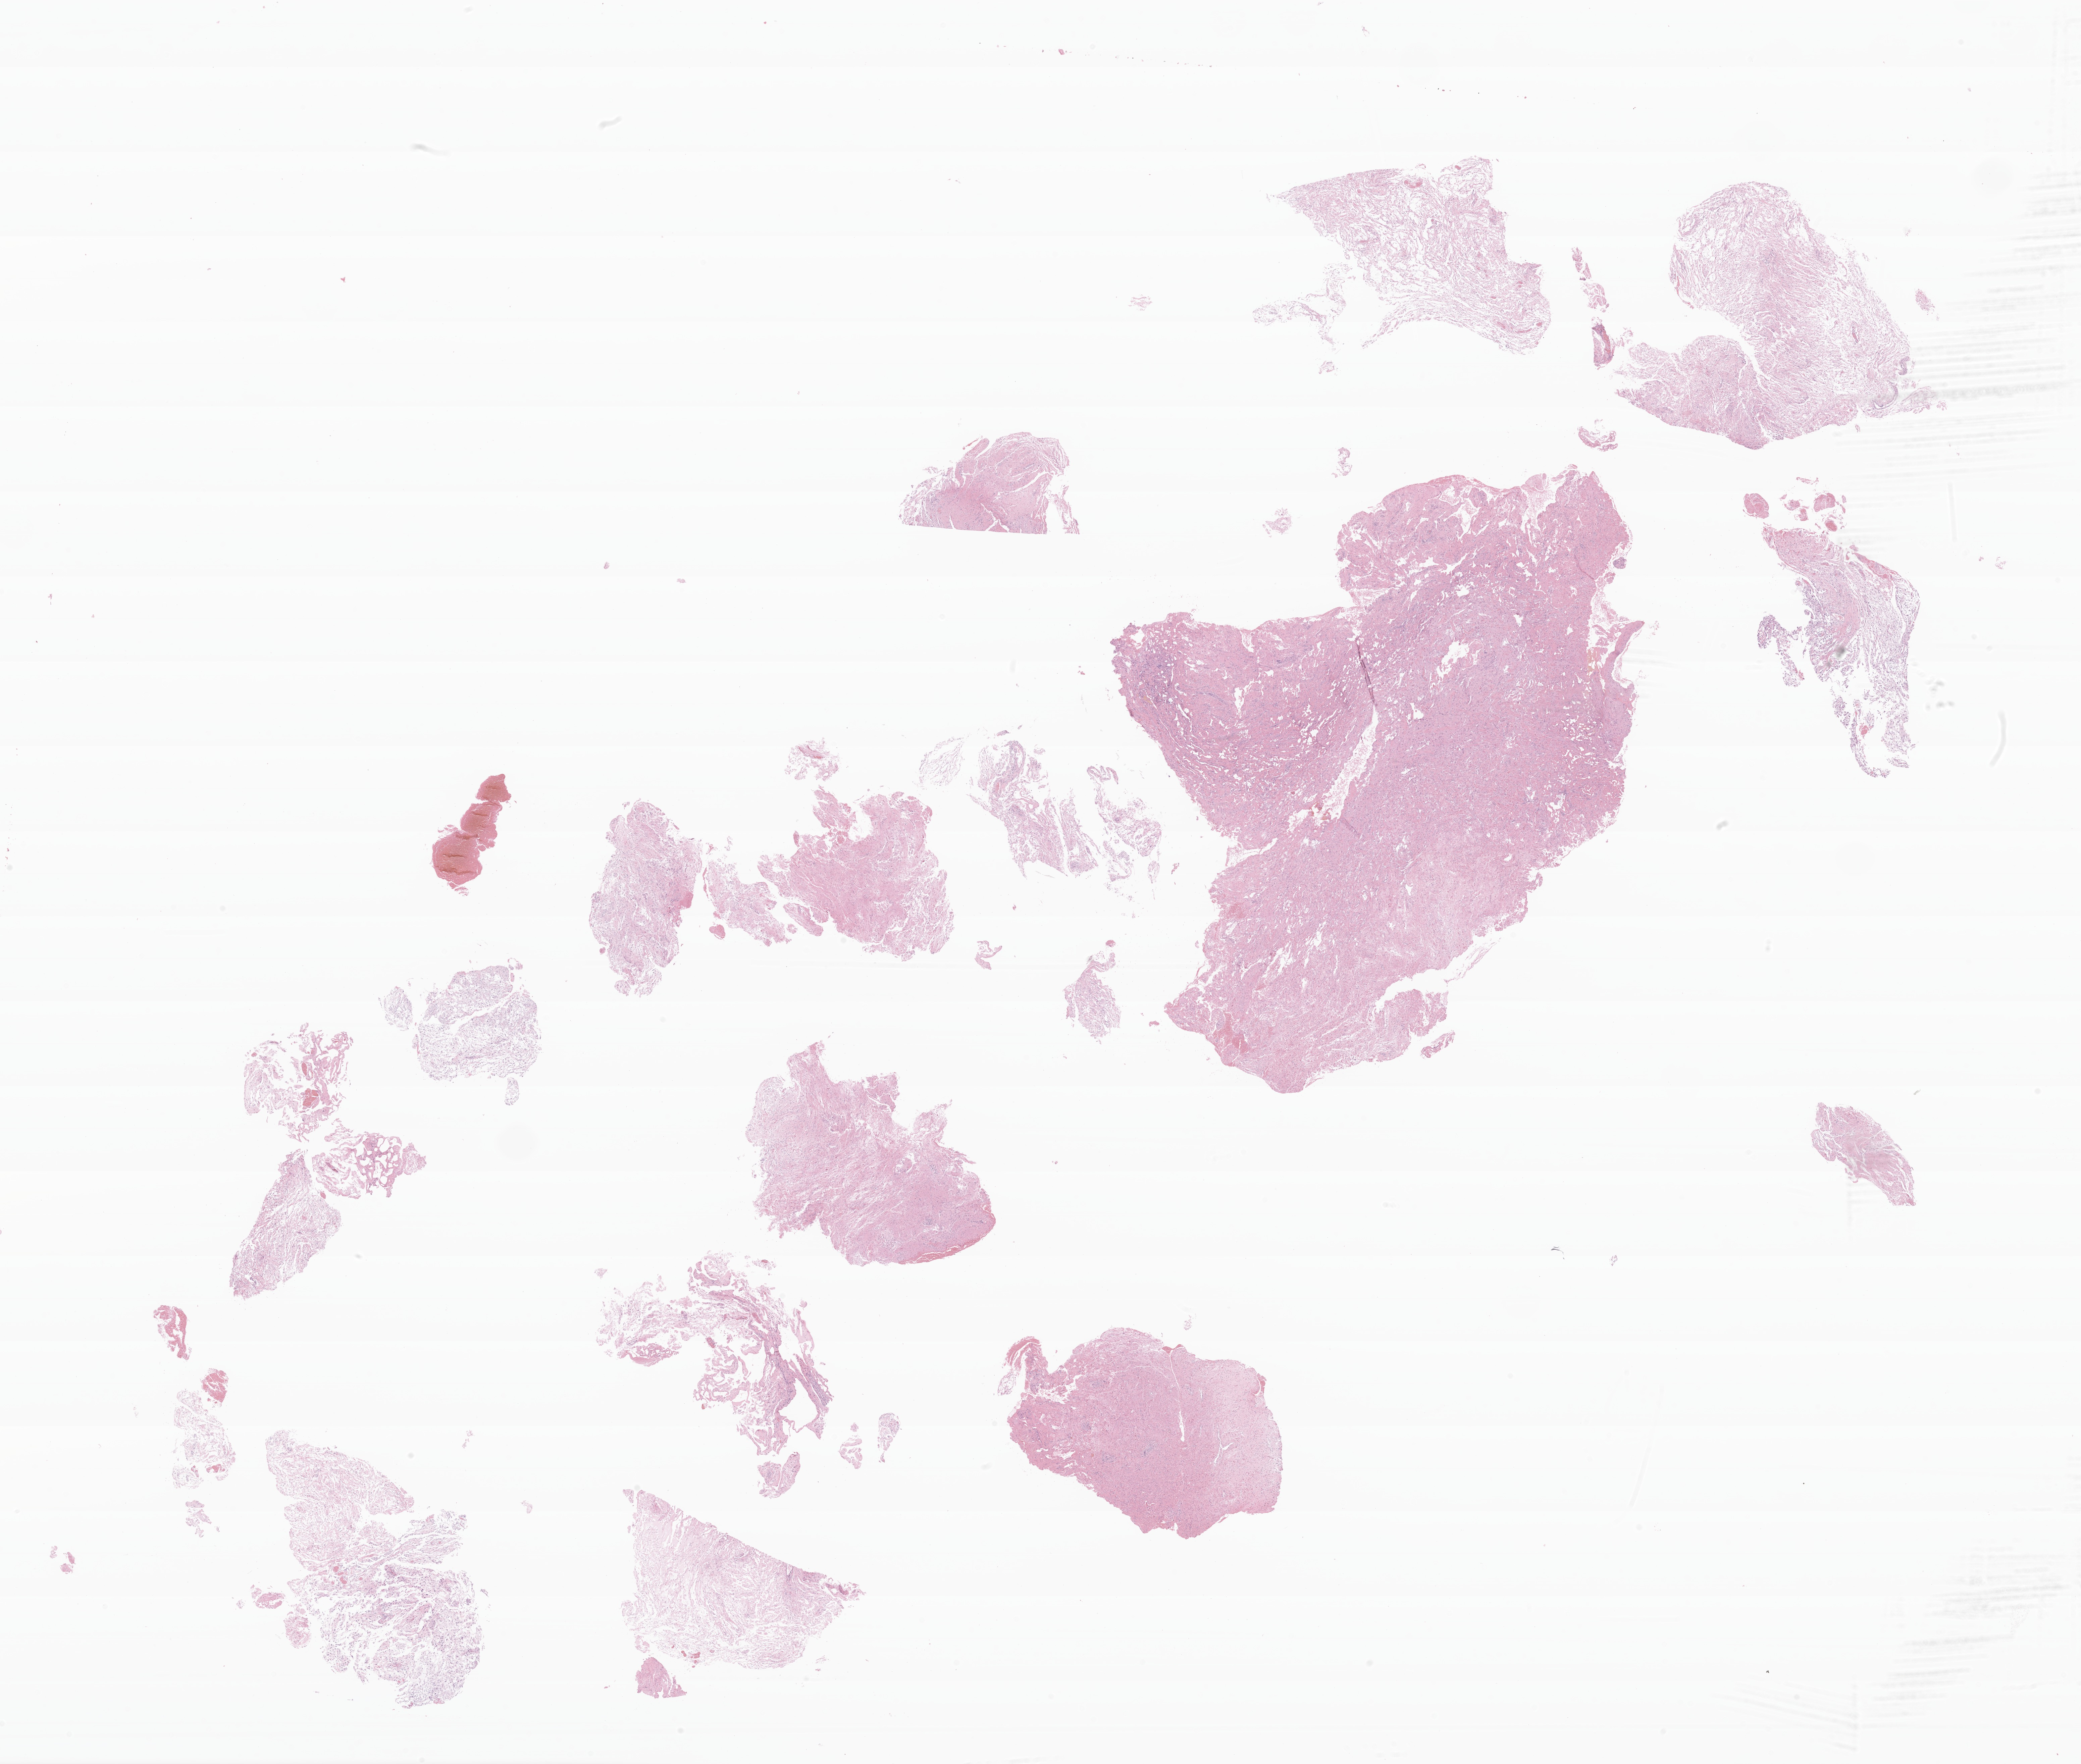
Digitized haematoxylin and eosin-stained section of tumor tissue from the cerebrum — a low-resolution overview of the entire scanned area, about 26.1 x 22.1 mm, formalin-fixed, paraffin-embedded (FFPE) tissue. Patient male; age 117 months (9 years 9 months).
Diagnosis (ICD-O-3 morphology term): Pilocytic astrocytoma.